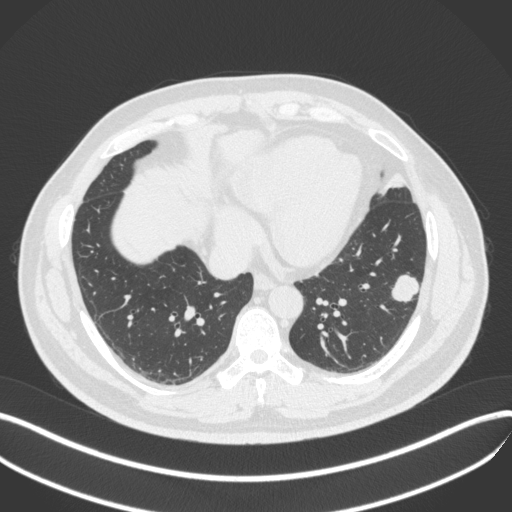
Chest CT, one axial slice; position 145 of 420 along the scan axis; reconstruction kernel B31f; 120 kVp; lung window (W 1500 / L -600 HU); 1 mm slice thickness; 512 × 512 image matrix, field of view 400 × 400 mm. Patient: male, 39 years. From the clinical record (not read from this slice): clinical TNM (as recorded): T2a N0 M0; histopathological grade: G2-3.
Annotated regions visible in this slice (bounding box drawn by a radiologist):
- lung tumour (recorded histology: adenocarcinoma): box from (x=386, y=268) to (x=423, y=308) px